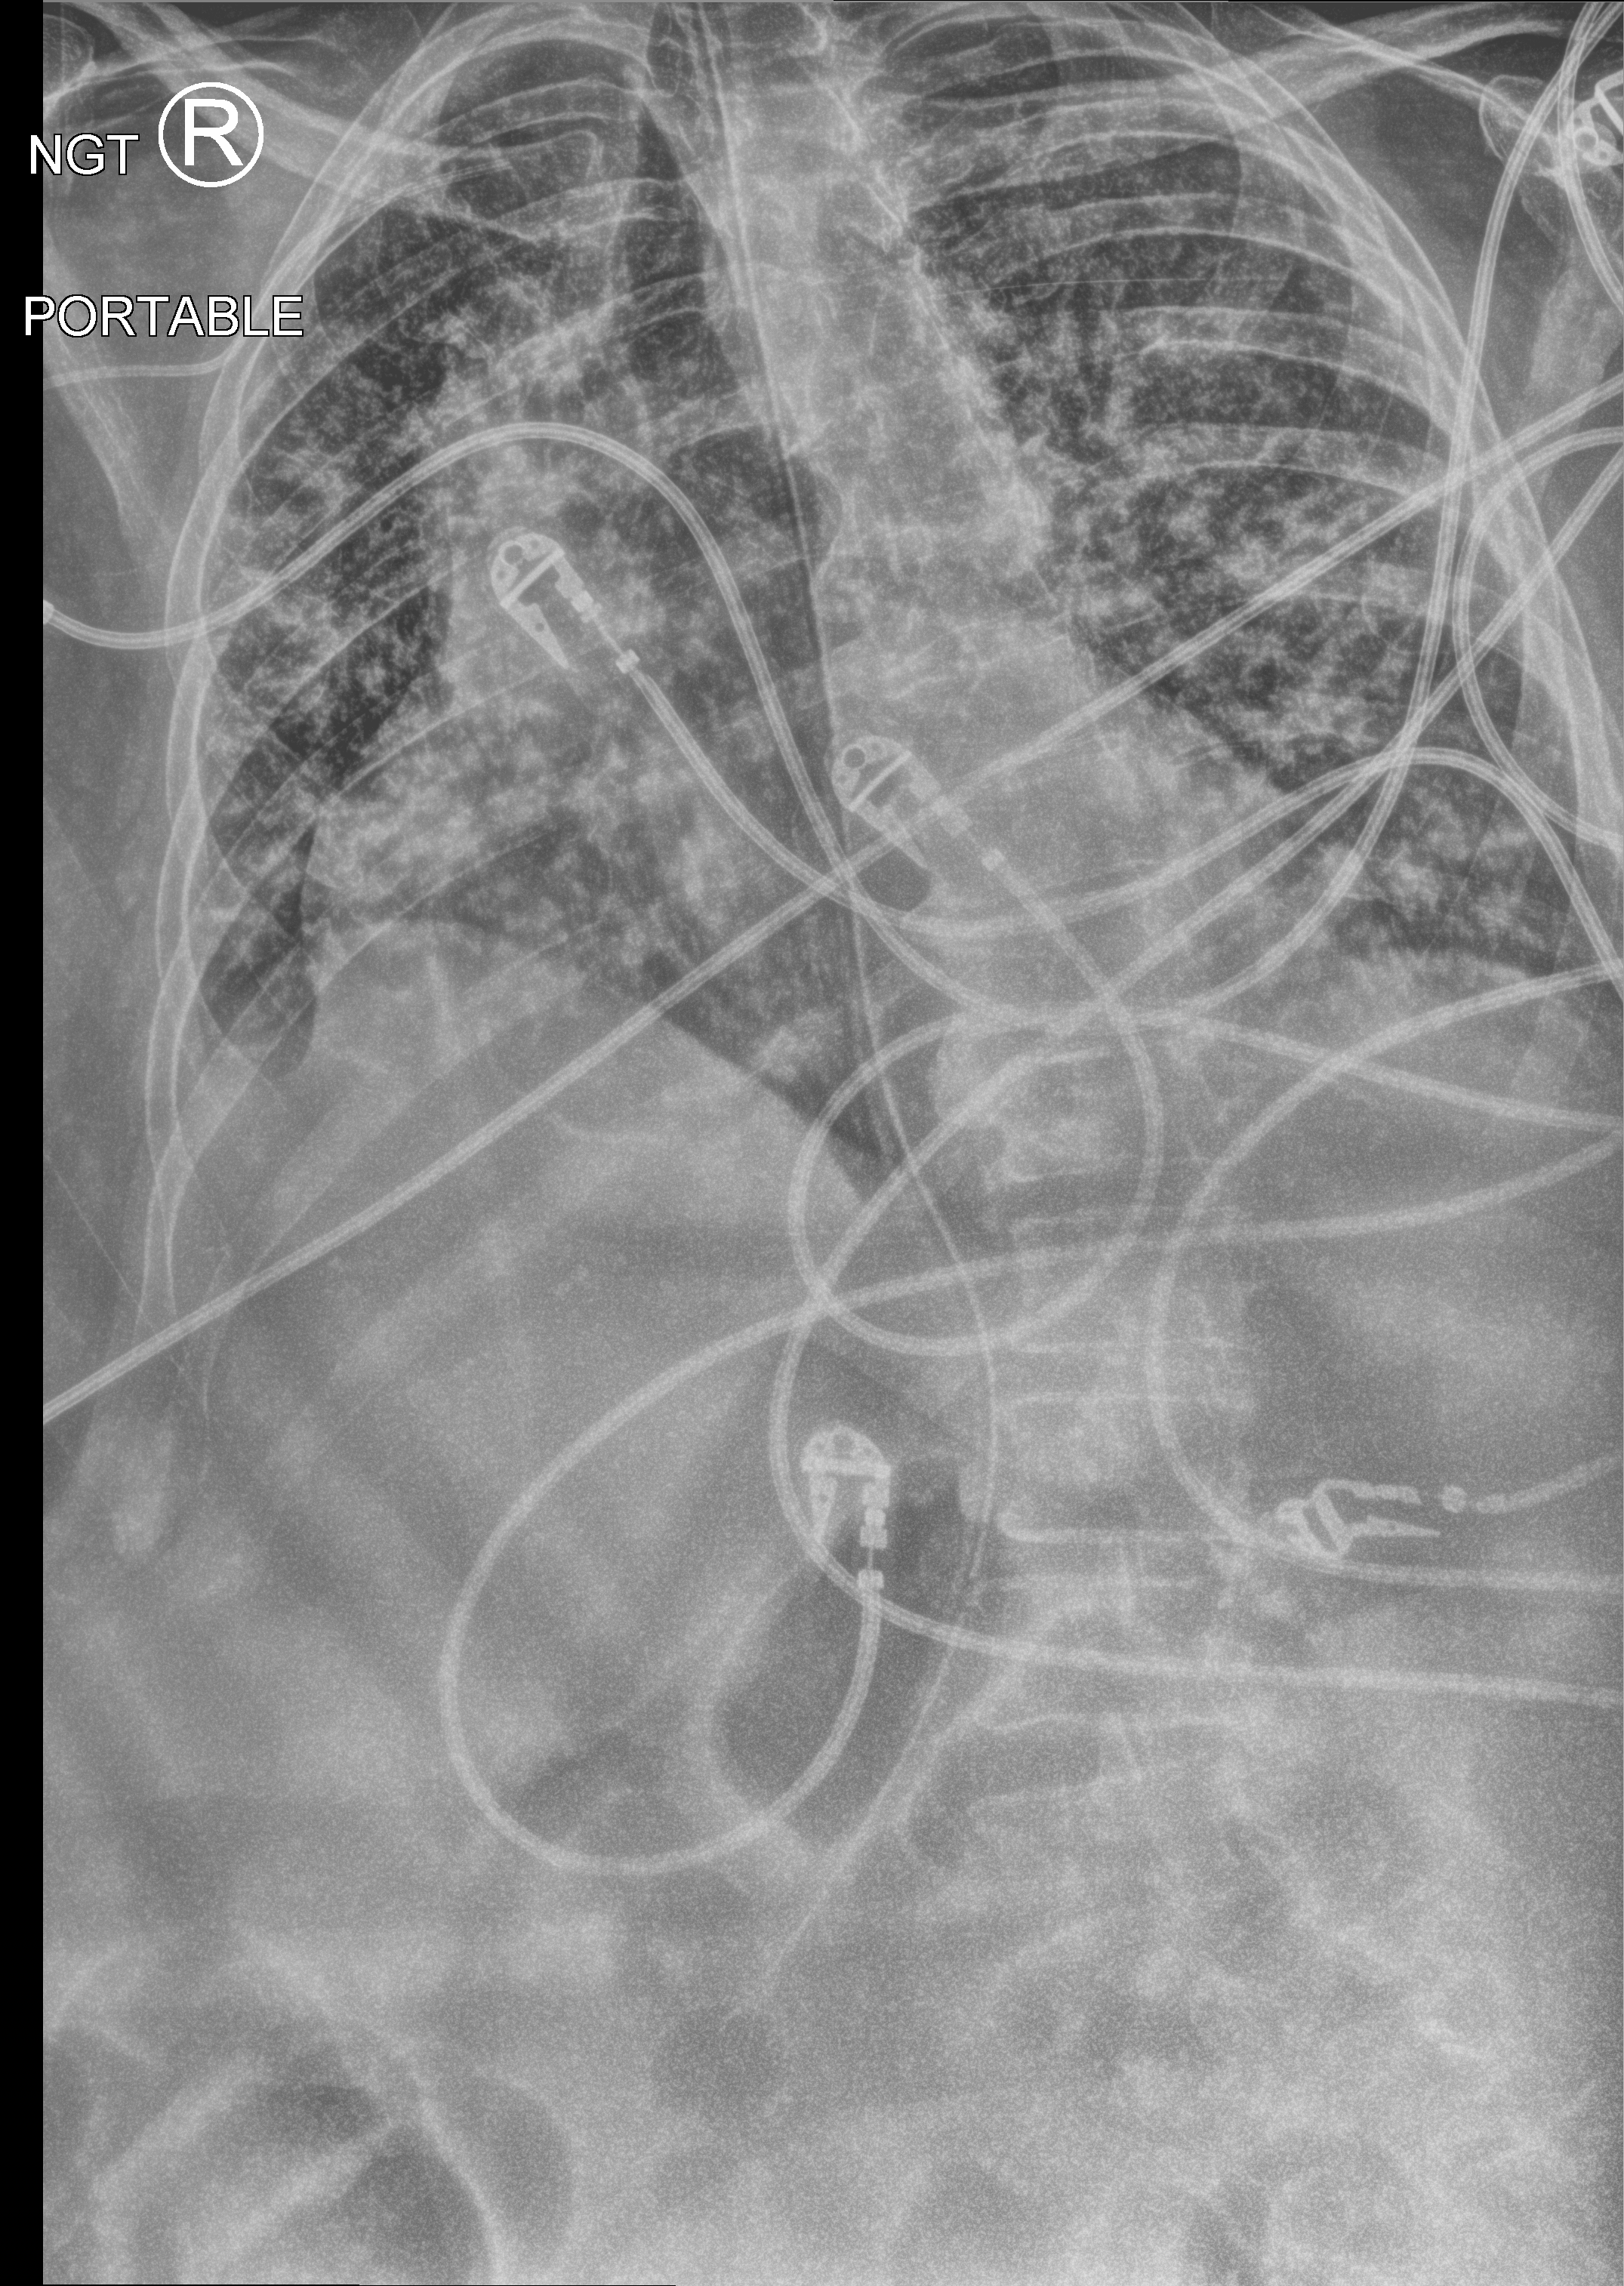
Chest X-ray (portable); anteroposterior (AP) projection. Female patient hospitalised with COVID-19, age 75–90 years.
Admission-level facts for this patient (not findings on this image; timing relative to this image not recorded): smoking status (admission record): former; mechanically ventilated during this hospital stay: yes.